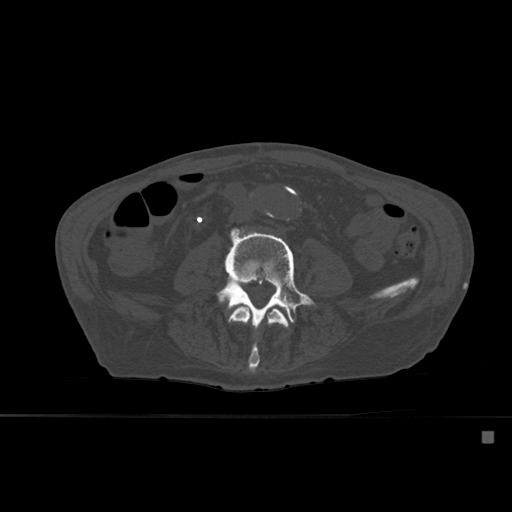
CT including the spine, one axial slice; bone window (W 1800 / L 400 HU); 1.5 mm slice thickness; 512 × 512 image matrix, field of view 373 × 373 mm. Patient: male, 78 years. From the clinical record (not read from this slice): primary cancer: prostate.
Outlined on this slice (semi-automatic segmentation, software-assisted and operator-edited):
- L3 vertebra: box from (x=228, y=306) to (x=289, y=374) px
- L4 vertebra: (x=215, y=227)–(x=317, y=329)